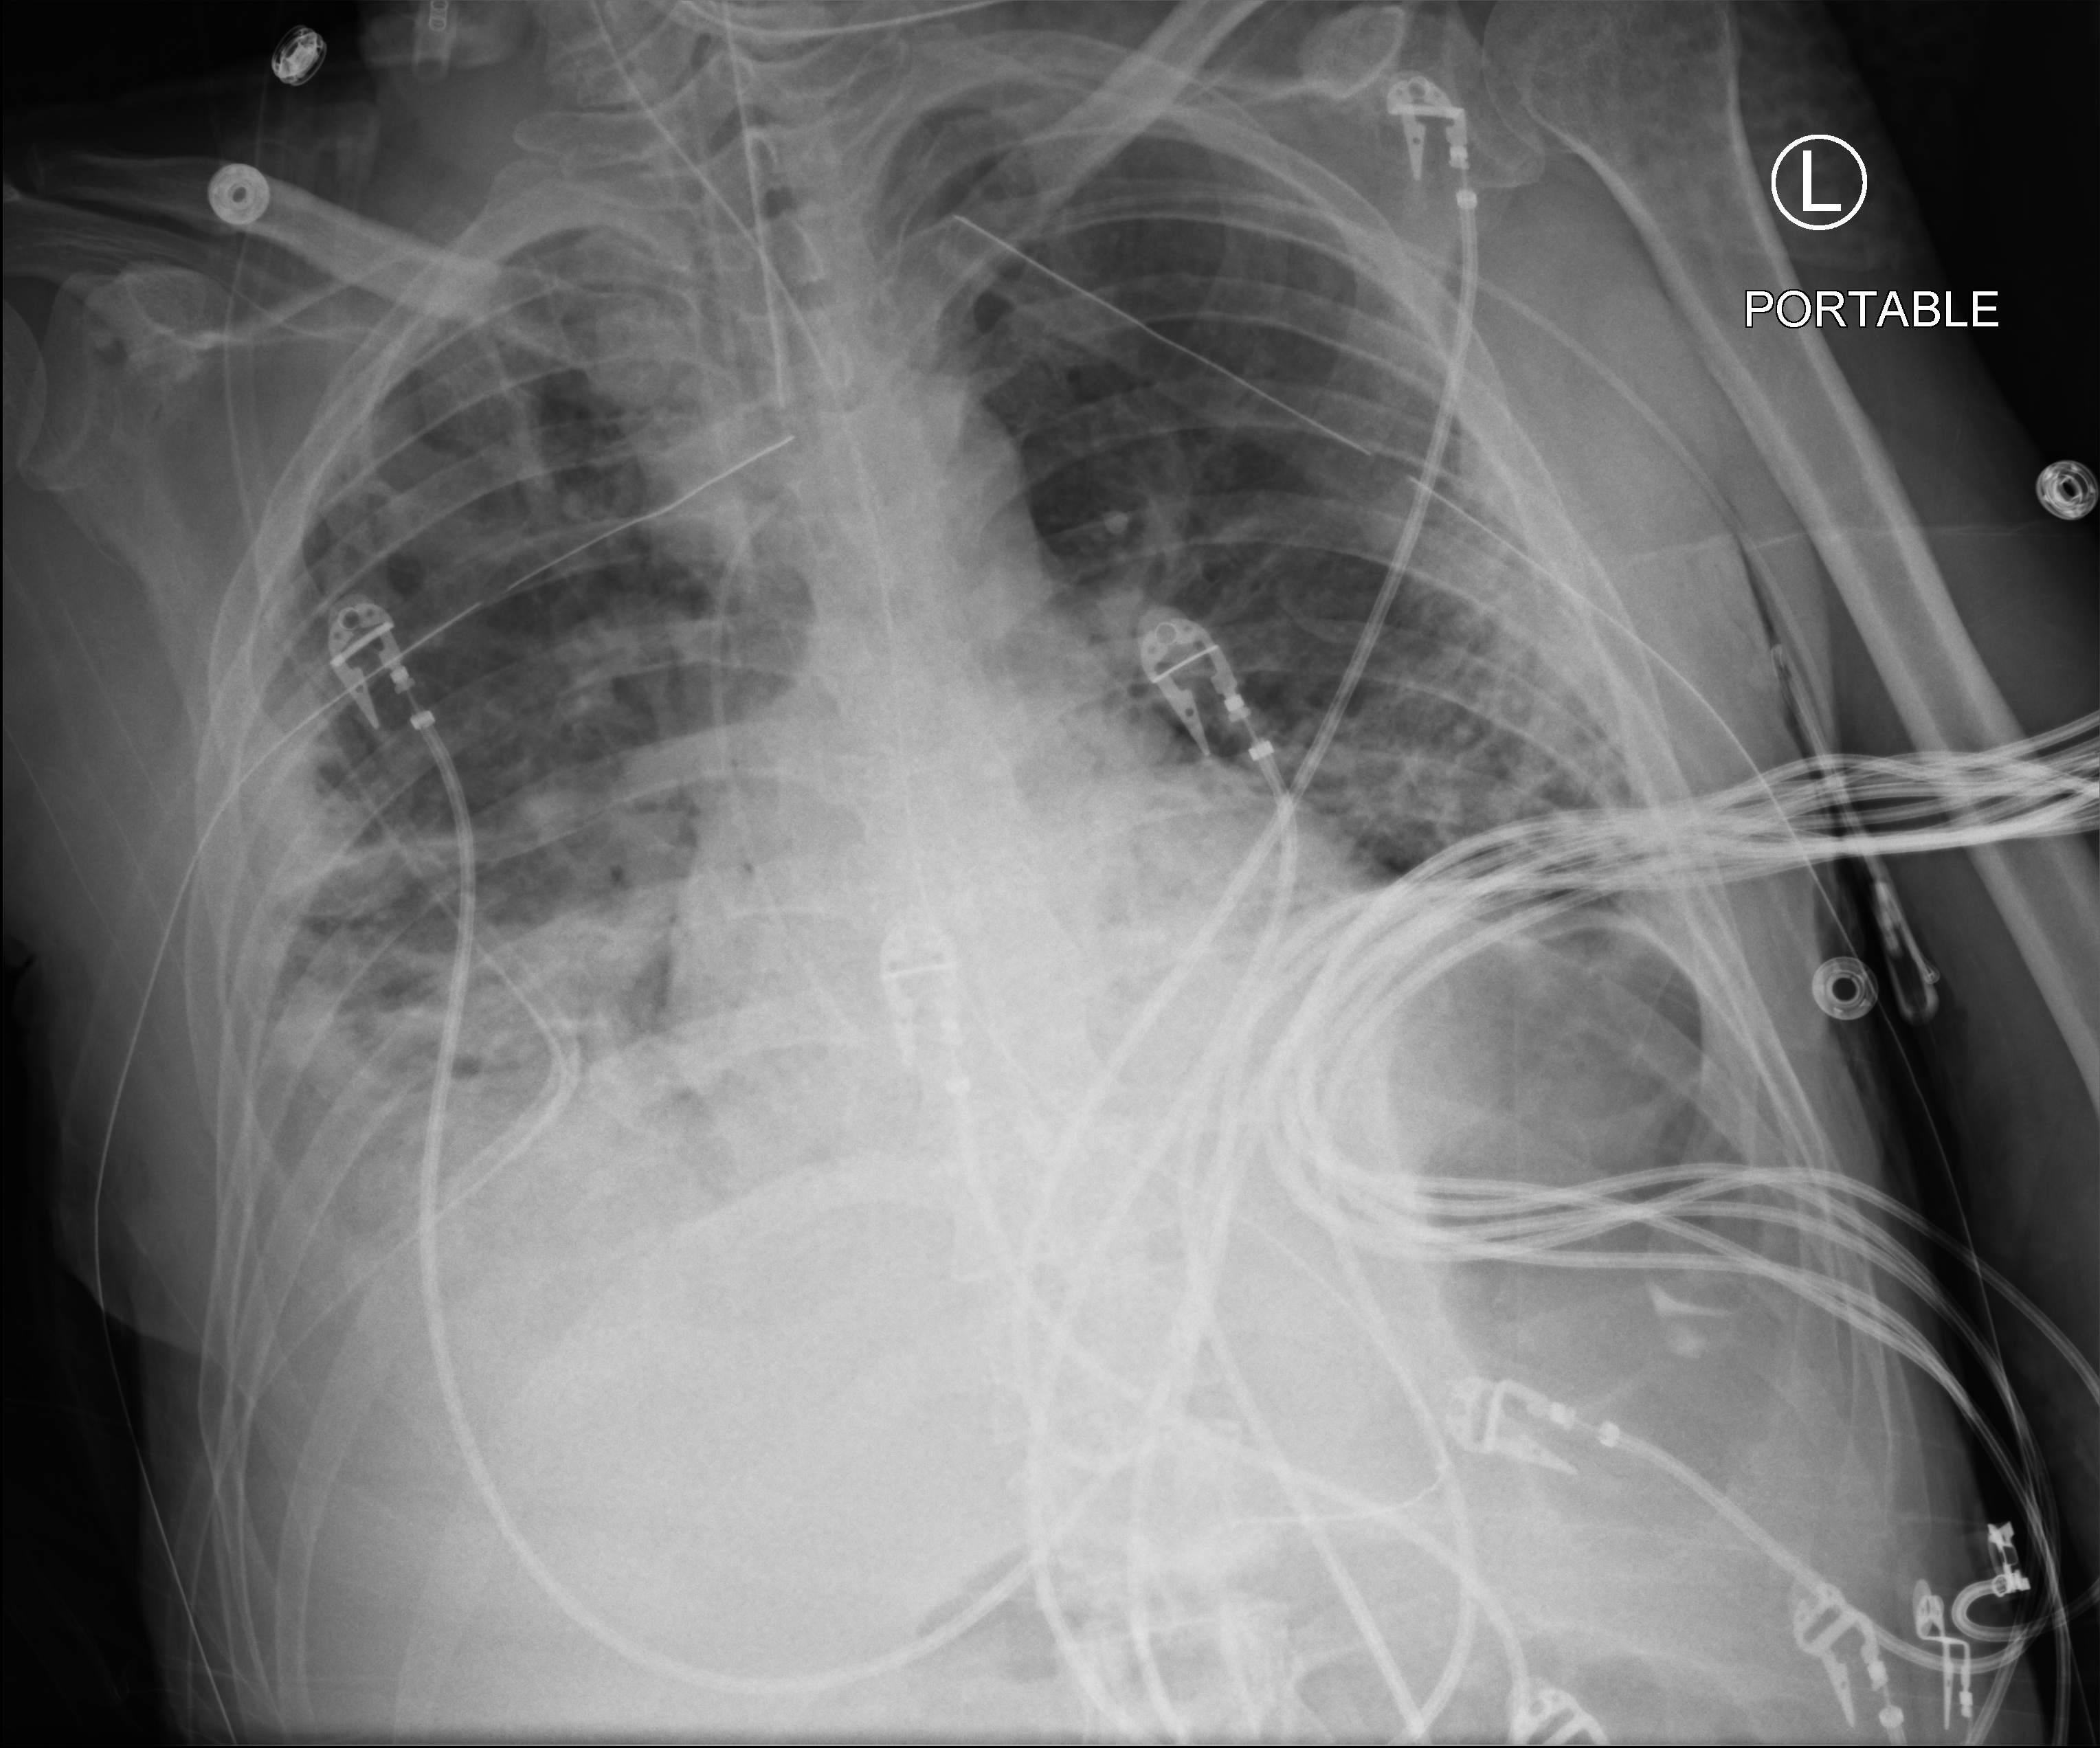
Chest X-ray (portable), anteroposterior (AP) projection. Patient hospitalised with COVID-19; male, aged 18–59 years.
From the hospital-stay record, not from the radiograph (when in the stay this image was taken is not recorded): mechanically ventilated during this hospital stay: yes.